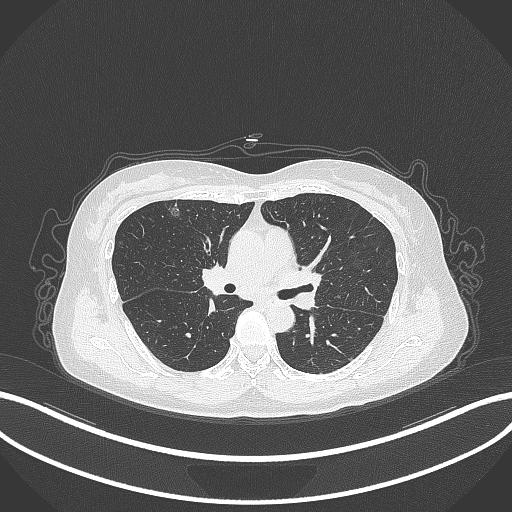
Chest CT, one axial slice. Position 193 of 315 along the scan axis. Reconstruction kernel B70f. Lung window (W 1500 / L -600 HU). 512 × 512 image matrix, field of view 400 × 400 mm. Female patient, age 61 years. From the clinical record (not read from this slice): clinical TNM (as recorded): T1b N0 M0; histopathological grade: G1.
Annotated regions visible in this slice (bounding box drawn by a radiologist):
- lung tumour (recorded histology: adenocarcinoma): bounding box <166,202,183,222> (left, top, right, bottom; pixels)